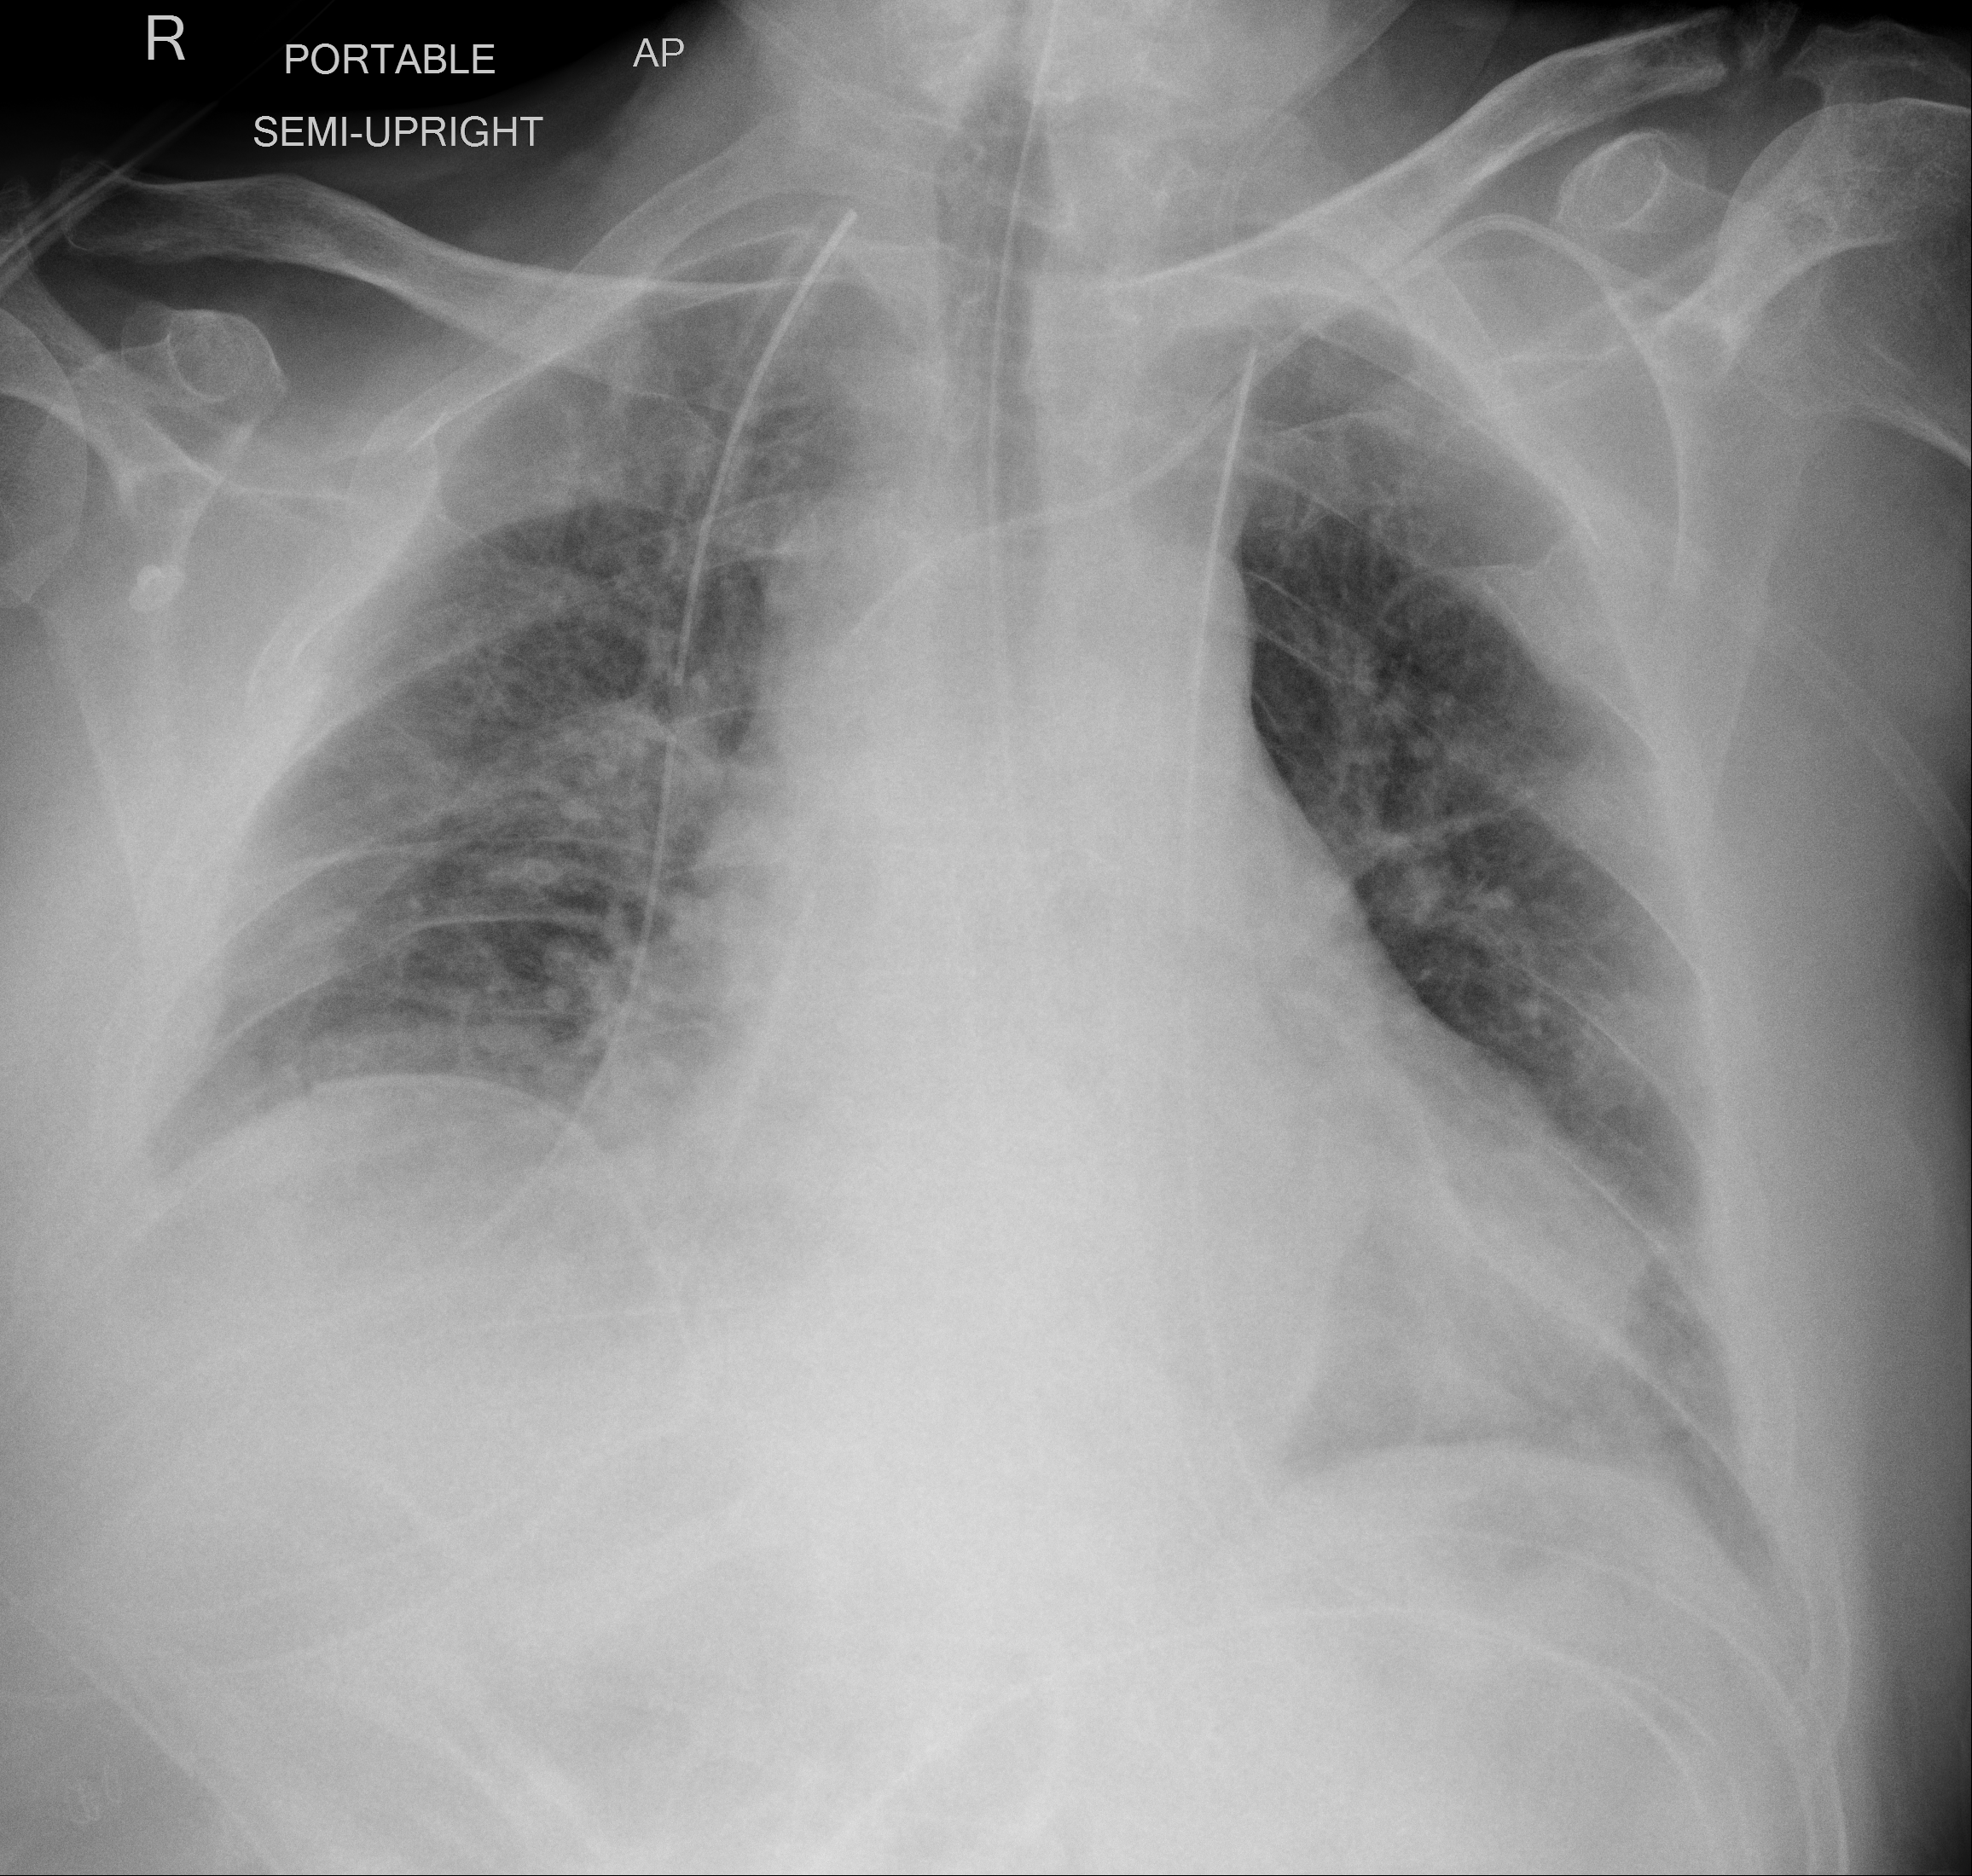
Chest X-ray (portable), AP projection. Male patient, age 64 years; imaged 3 days after the COVID-19 diagnosis.
Radiologist key findings (as recorded): Lungs are underinflated with patchy and streaky airspace opacities along the lung bases and mid right lung region.